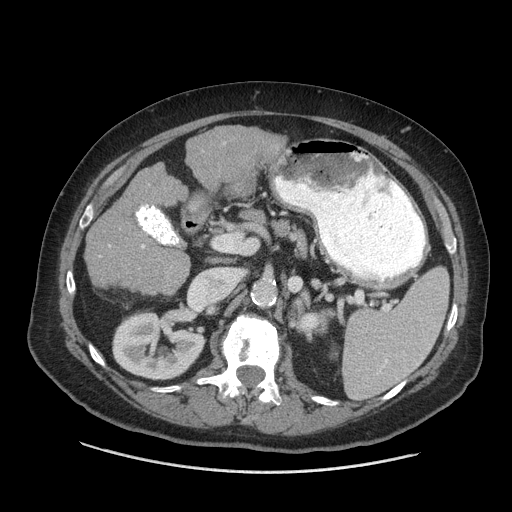
Contrast-enhanced abdominal CT (liver protocol), one axial slice. Position 29 of 77 along the scan axis. Reconstruction kernel STANDARD. 140 kVp. Soft-tissue window (W 400 / L 40 HU). 512 × 512 image matrix. Case-level facts recorded for this patient, not image findings: diagnosis: hepatocellular carcinoma (patient treated with transarterial chemoembolisation; whether this scan precedes or follows treatment is not stated here); TNM stage (as recorded): Stage-I; Child-Pugh class: A; tumour differentiation: well differentiated; tumour nodularity: uninodular.
Annotated regions visible in this slice (semi-automatic segmentation, software-assisted and operator-edited):
- liver parenchyma outside the tumour (the mass and vessels are separate outlines, so this box may not span the whole liver): bounding box [x1, y1, x2, y2] px = [86, 126, 284, 284]
- liver vessels: [142, 245, 145, 248]